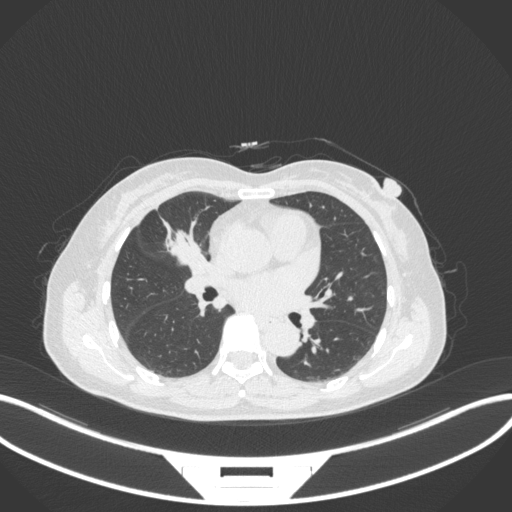
Chest CT, one axial slice; position 158 of 282 along the scan axis; reconstruction kernel B31f; lung window (W 1500 / L -600 HU); 1 mm slice thickness; 512 × 512 image matrix. Female patient, age 51 years. From the clinical record (not read from this slice): clinical TNM (as recorded): T1c N0 M0; histopathological grade: G2.
Outlined on this slice (bounding box drawn by a radiologist):
- lung tumour (recorded histology: adenocarcinoma): bounding box [x1, y1, x2, y2] px = [162, 216, 204, 267]